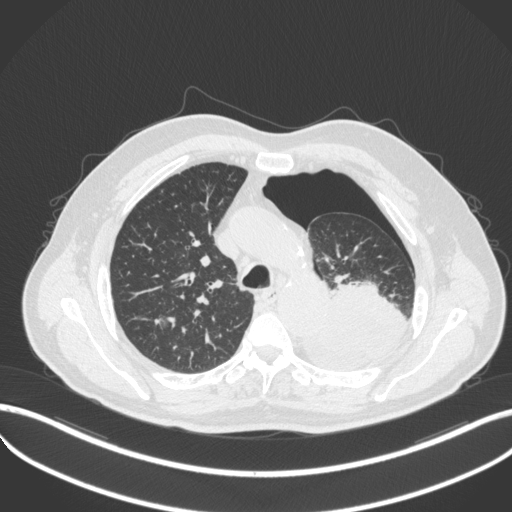
Chest CT, one axial slice; slice 369 of 466 in the series (ordered by position); 120 kVp; lung window (W 1500 / L -600 HU); 1 mm slice thickness; 512 × 512 image matrix. Male patient, age 76 years. From the clinical record (not read from this slice): clinical TNM (as recorded): T3 N0 M1b.
Annotated regions visible in this slice (rectangle marked by the reading radiologist):
- lung tumour (recorded histology: adenocarcinoma): box from (x=310, y=278) to (x=412, y=367) px